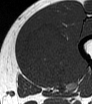
MRI of an extremity soft-tissue mass, one axial slice; slice 21 of 62 in the series (ordered by position); MR volume resampled by the dataset authors to the PET/CT grid (not the native acquisition matrix); 92 × 104 image matrix. Male patient. From the clinical record (not read from this slice): histological type: mixoid liposarcoma; grade: low; site of the primary tumour: left thigh.
Structures marked on this image (expert contour drawn on MRI and transferred to this co-registered scan by the dataset authors):
- gross tumour volume (mass): bounding box [x1, y1, x2, y2] px = [21, 22, 68, 84]